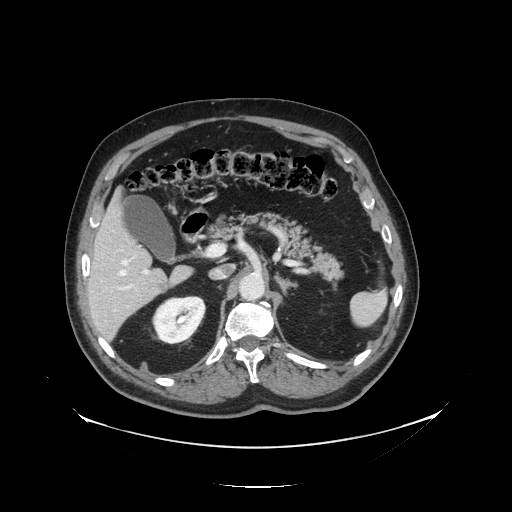
Contrast-enhanced abdominal CT, one axial slice; slice 76 of 138 in the series (ordered by position); 120 kVp; intravenous contrast given; soft-tissue window (W 400 / L 40 HU); 2.5 mm slice thickness; 512 × 512 image matrix. Male patient, age 77 years. From the clinical record (not read from this slice): diagnosis: colorectal cancer liver metastases, imaged before liver resection; multiple liver metastases: no; largest metastasis: 1.5 cm; disease in both lobes: no.
Structures marked on this image (outlined manually by an expert reader):
- hepatic veins: bounding box <119,260,128,276> (left, top, right, bottom; pixels)
- liver: <86,195,191,340>
- planned liver remnant (the part of the liver to remain after resection): <87,197,154,287>
- portal vein (with intrahepatic branches): <116,269,150,290>
- liver metastasis: <158,283,167,292>